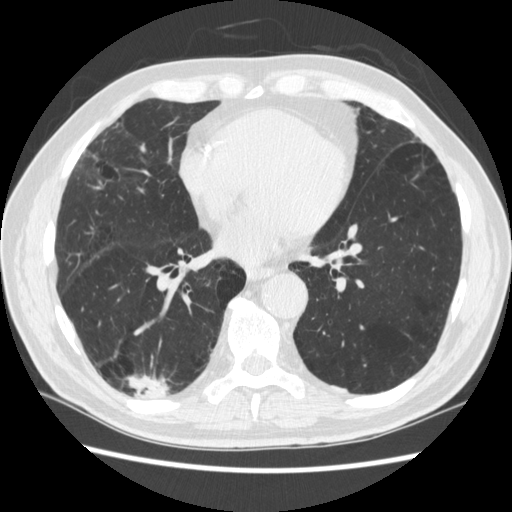
Low-dose screening chest CT, one axial slice; slice 115 of 266 in the series (ordered by position); reconstruction kernel STANDARD; 120 kVp; lung window (W 1500 / L -600 HU); 1.25 mm slice thickness; 512 × 512 image matrix, field of view 360 × 360 mm.
Annotated regions visible in this slice (expert manual segmentation):
- lesion 1 (tumor, upper lobe of right lung): box from (x=129, y=376) to (x=168, y=399) px